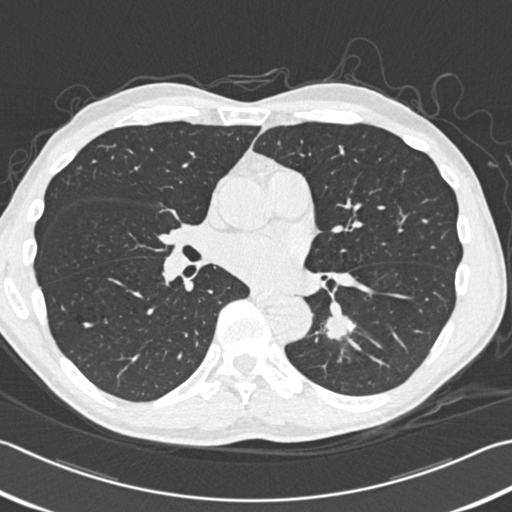
Low-dose screening chest CT, one axial slice; slice 178 of 354 in the series (ordered by position); 120 kVp; lung window (W 1500 / L -600 HU); 512 × 512 image matrix, field of view 346 × 346 mm.
Annotated regions visible in this slice (outlined manually by an expert reader):
- lesion 1 (tumor, lower lobe of left lung): box from (x=326, y=315) to (x=355, y=340) px